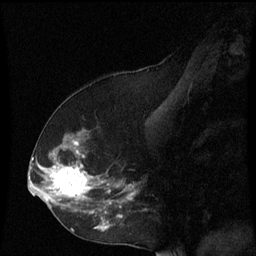
Breast MRI (dynamic contrast-enhanced), one sagittal slice; position 32 of 60 along the scan axis; dynamic contrast-enhanced series, image 2 of 3 at this slice position (ordered by acquisition); 1.5 T; TE 4.2 ms, TR 8.9 ms; 2 mm slice thickness; 256 × 256 image matrix, field of view 200 × 200 mm. Female patient, age 53 years. Case-level facts recorded for this patient, not image findings: setting: breast cancer imaged before/during neoadjuvant chemotherapy; receptor status: HR-positive, HER2-negative.
Structures marked on this image (semi-automatic segmentation, software-assisted and operator-edited):
- analysis volume of interest (the breast-tissue region the enhancement analysis was run in; not a lesion): box from (x=38, y=128) to (x=137, y=231) px
- tumour enhancement mask (voxels above the 70 % enhancement threshold inside the analysis volume of interest): (x=40, y=142)–(x=135, y=231)